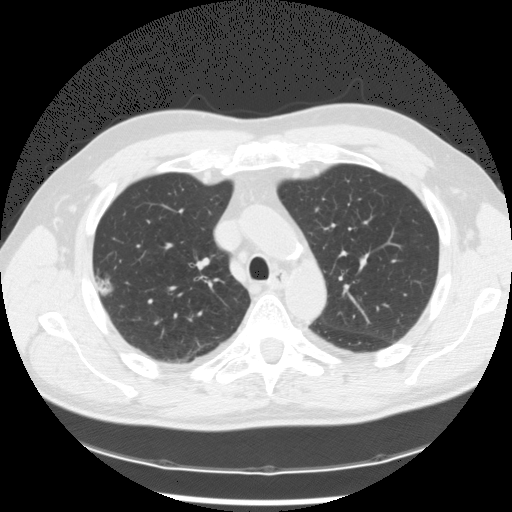
Low-dose screening chest CT, axial slice. First (baseline) screen. Lung window (W 1500 / L -600 HU). Slice 38 of 119 in the series. 512 × 512 image matrix, field of view 360 × 360 mm. Male participant, aged 62 years at enrolment. Former smoker at enrolment.
Expert reader's lesion annotation, box from (x=89, y=270) to (x=119, y=301) px. Reader record for this screening exam (exam-level; its link to the box is not recorded): non-calcified nodule or mass ≥4 mm, right upper lobe, 14 × 11 mm, poorly defined margins, mixed attenuation. Lung cancer was diagnosed 343 days after this screen (after the second annual screen): adenocarcinoma, NOS, right upper lobe, poorly differentiated (G3), stage IIB (AJCC 6th edition), 5 mm at pathology.